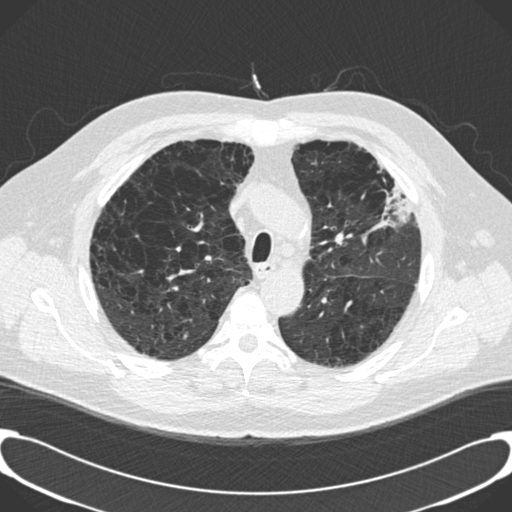
Low-dose screening chest CT, one axial slice; position 145 of 189 along the scan axis; 120 kVp; lung window (W 1500 / L -600 HU); 2 mm slice thickness; 512 × 512 image matrix.
Structures marked on this image (outlined manually by an expert reader):
- lesion 1 (tumor, upper lobe of left lung): box from (x=383, y=184) to (x=410, y=227) px